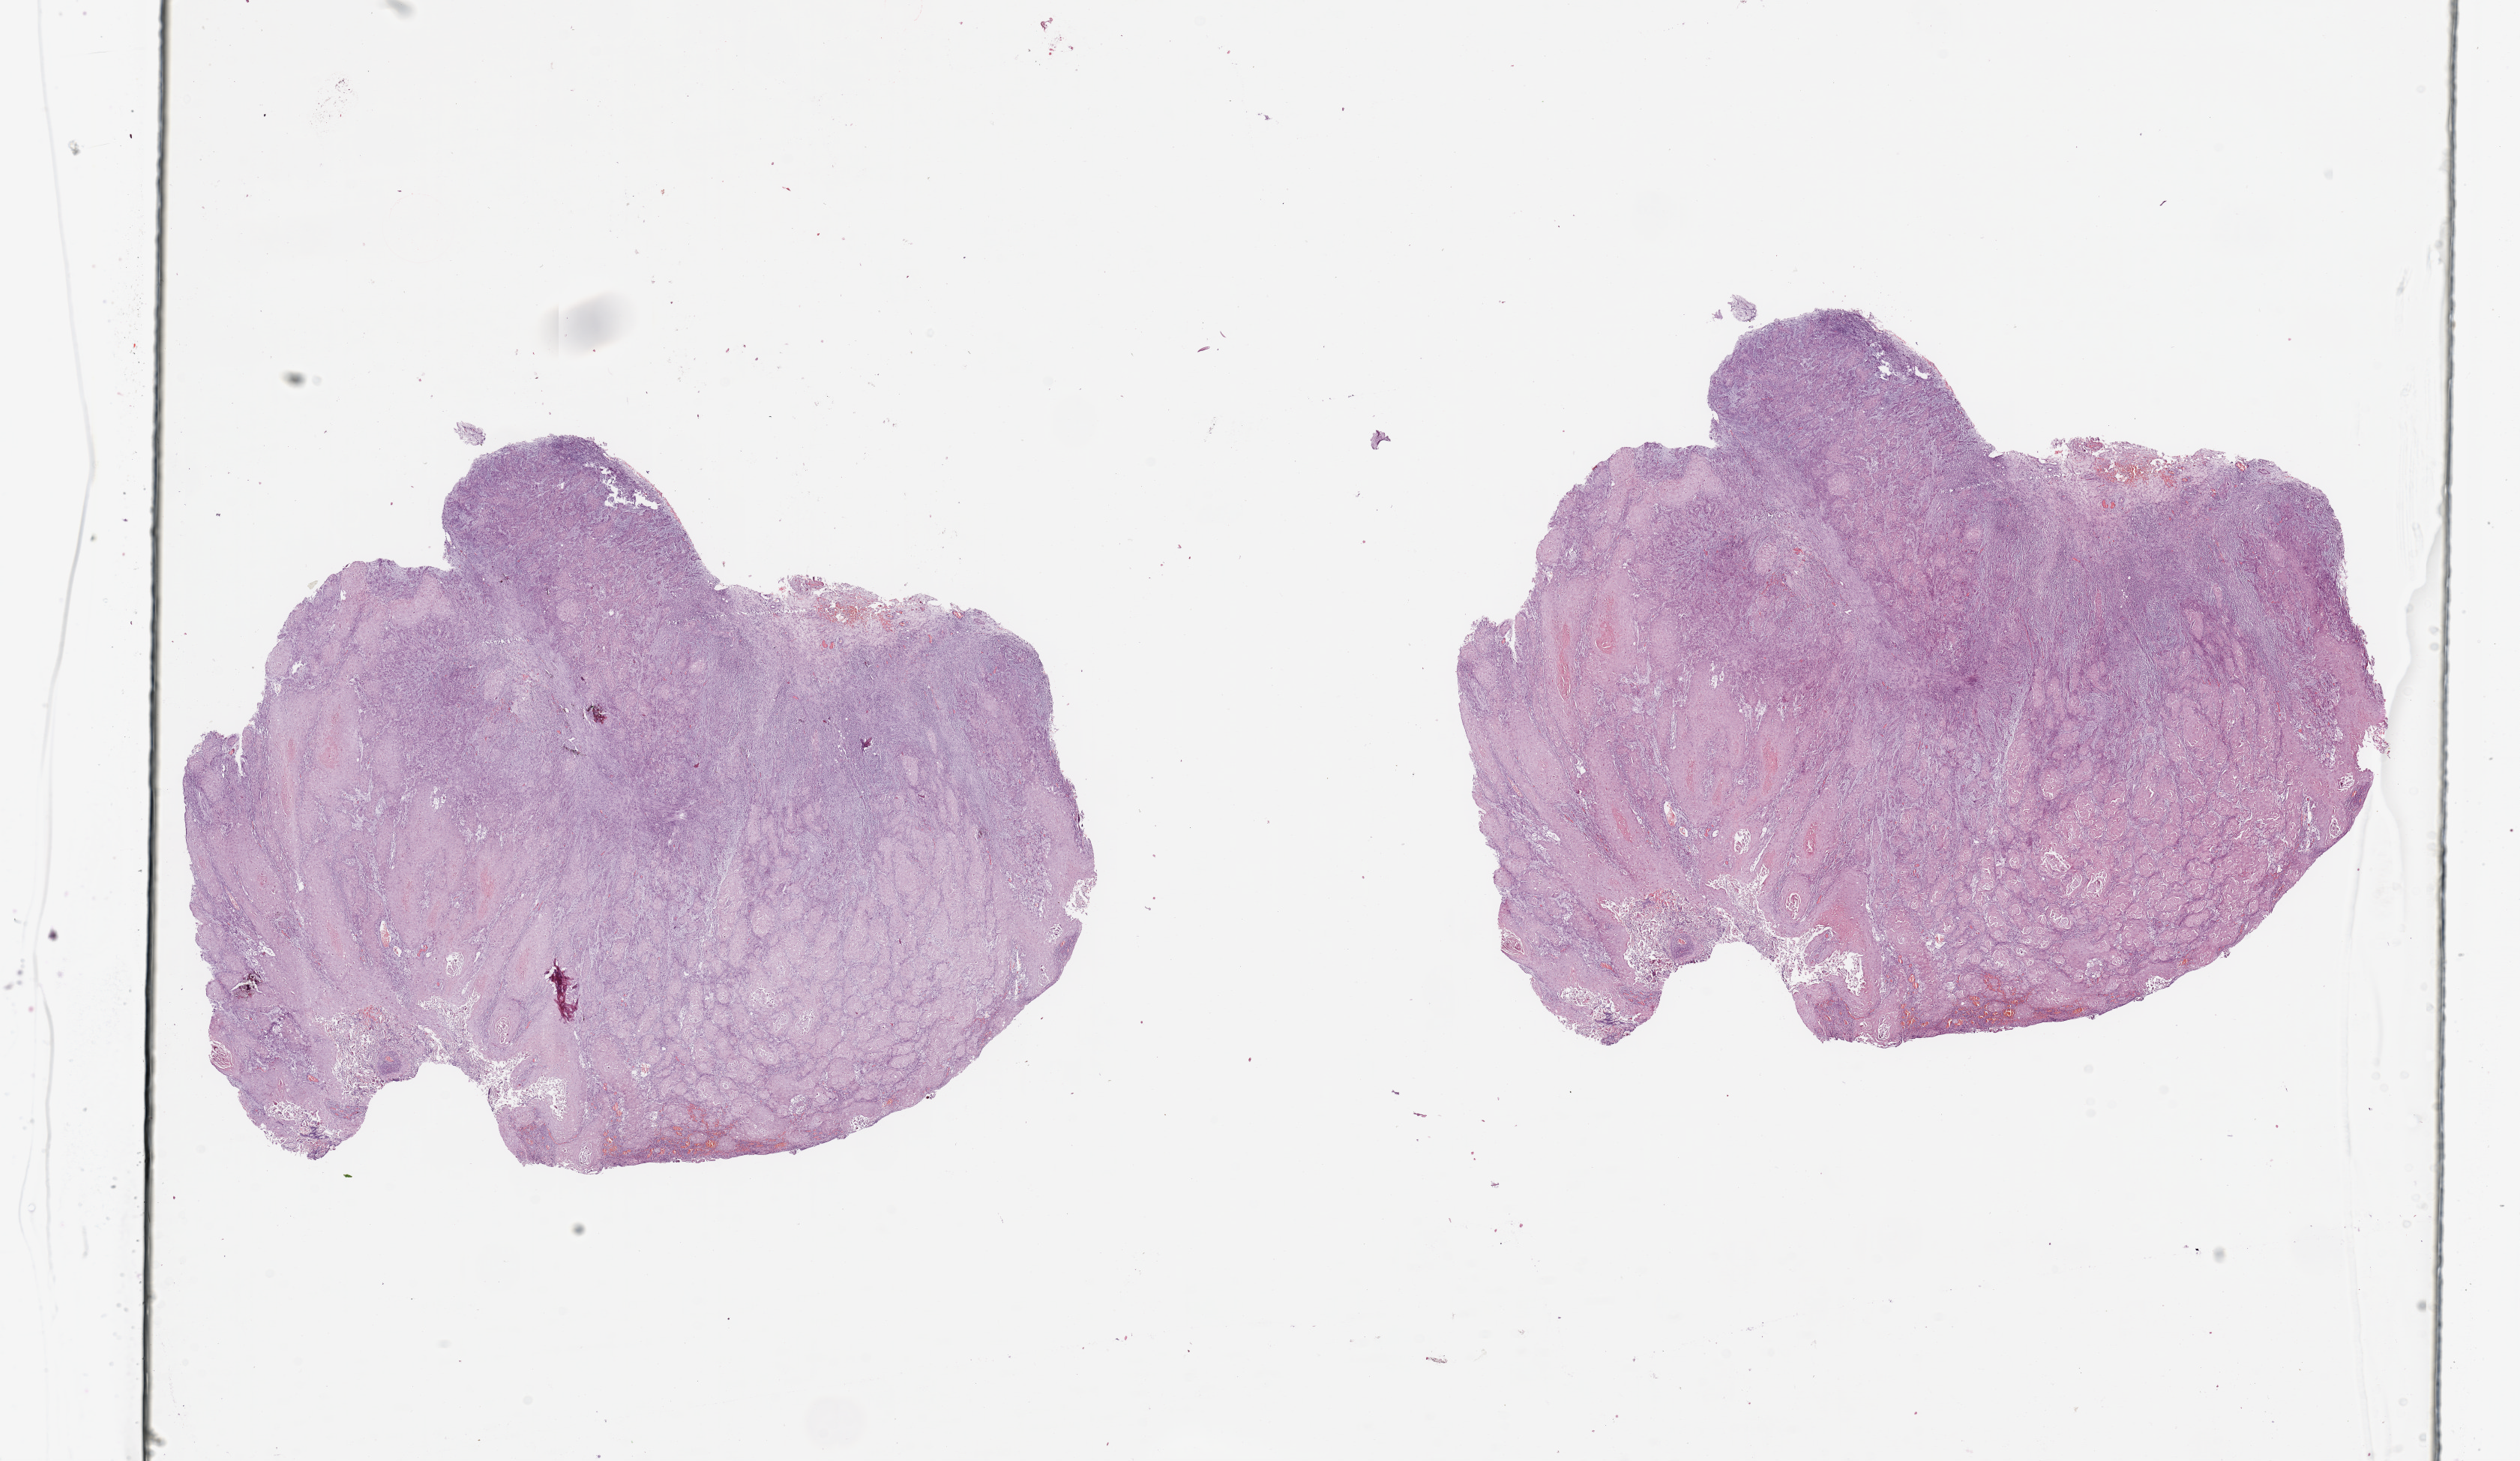
Digitized H&E tissue section (whole slide) — shown as a low-resolution overview of the whole scanned area (about 26.6 x 15.4 mm), tumour tissue sample, sampled site: floor of mouth. Patient: female, age 70 years. Histologic grade: G2 (moderately differentiated). Pathologist review of this section (percent, as recorded): tumour nuclei 85%, necrosis 2%.
Primary tumour site (as recorded): oral cavity. AJCC pathologic stage: III. Diagnosis: Squamous cell carcinoma, NOS.